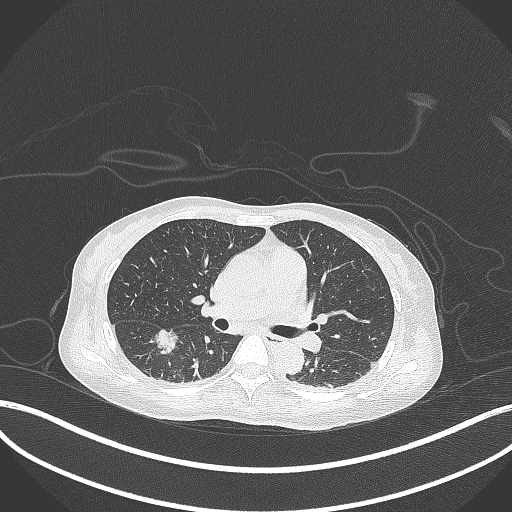
Chest CT, one axial slice. Reconstruction kernel B70f. Lung window (W 1500 / L -600 HU). 1 mm slice thickness. 512 × 512 image matrix, field of view 400 × 400 mm. Female patient, age 44 years. Case-level facts recorded for this patient, not image findings: clinical TNM (as recorded): T1c N0 M0.
Structures marked on this image (bounding box drawn by a radiologist):
- lung tumour (recorded histology: adenocarcinoma): box from (x=153, y=327) to (x=176, y=354) px